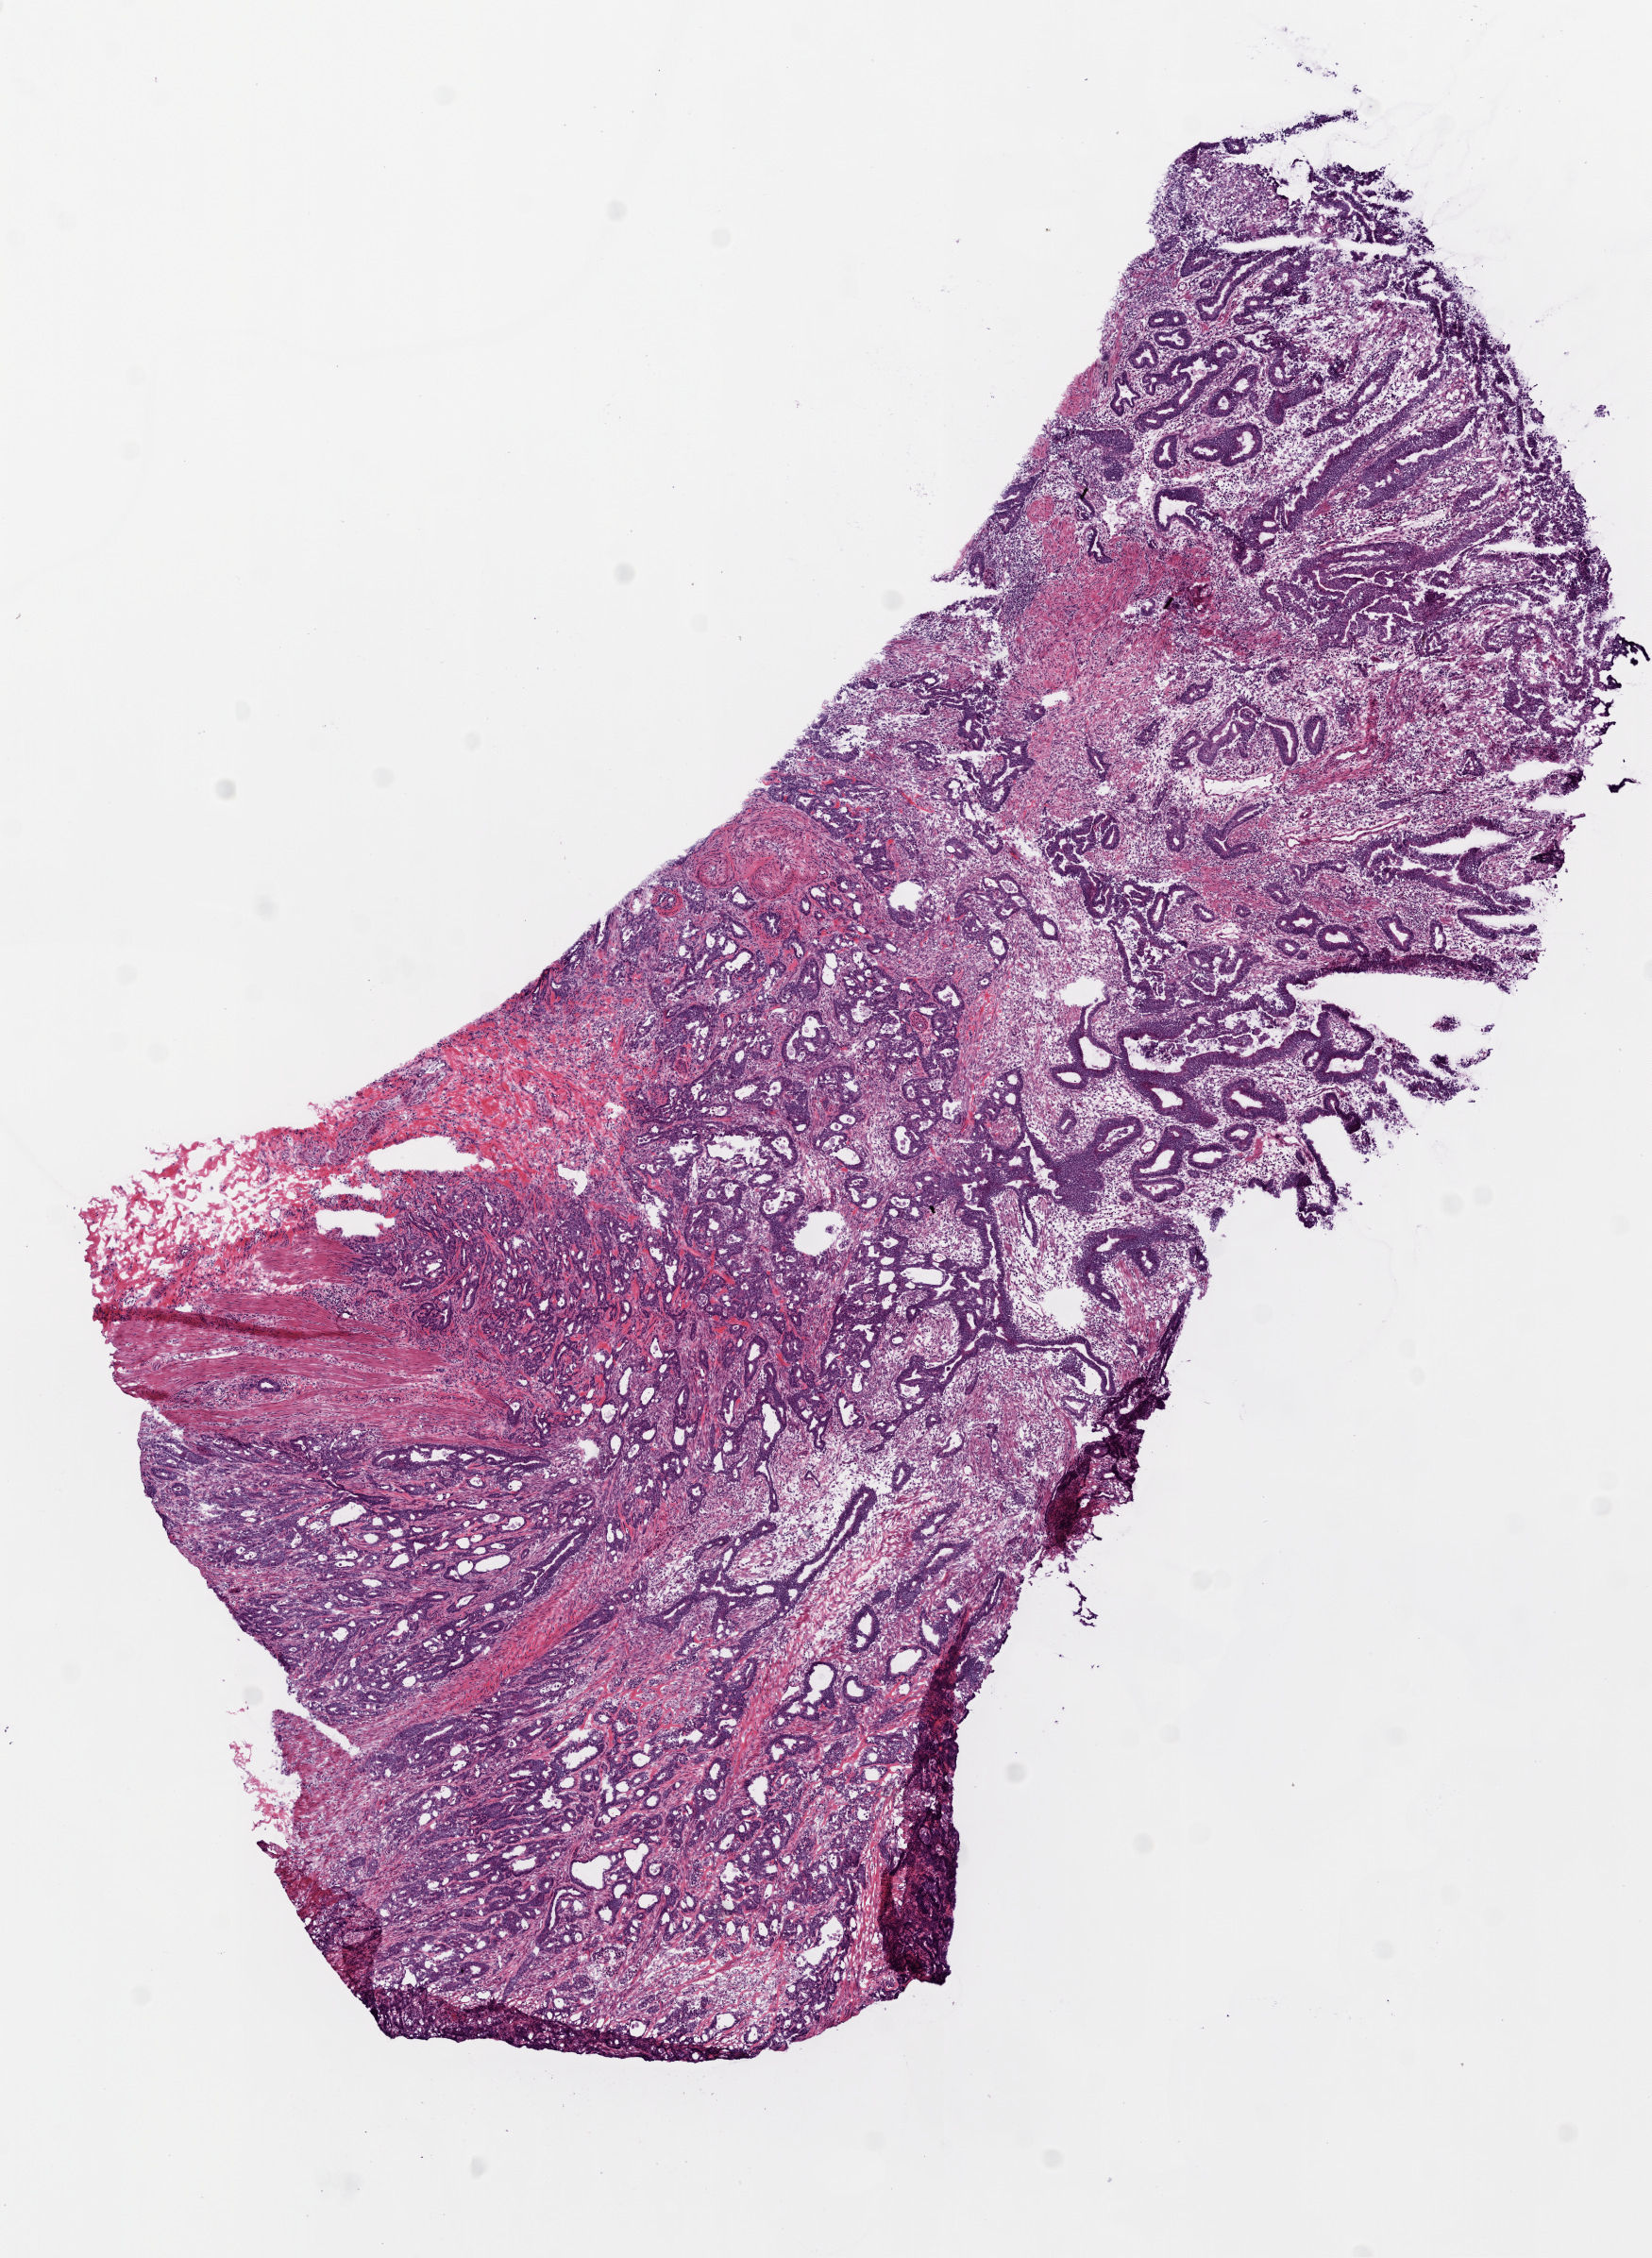
Whole-slide histology image, H&E-stained — whole scanned area (about 7.0 x 9.6 mm, acquisition: 20x scan) shown as a low-resolution overview, frozen section, primary tumour sample from the rectum. Male, age 73 years at initial diagnosis. Pathologist review of this section (percent, as recorded): tumour cells 75%, tumour nuclei 70%.
Histologic diagnosis: Adenocarcinoma, NOS.